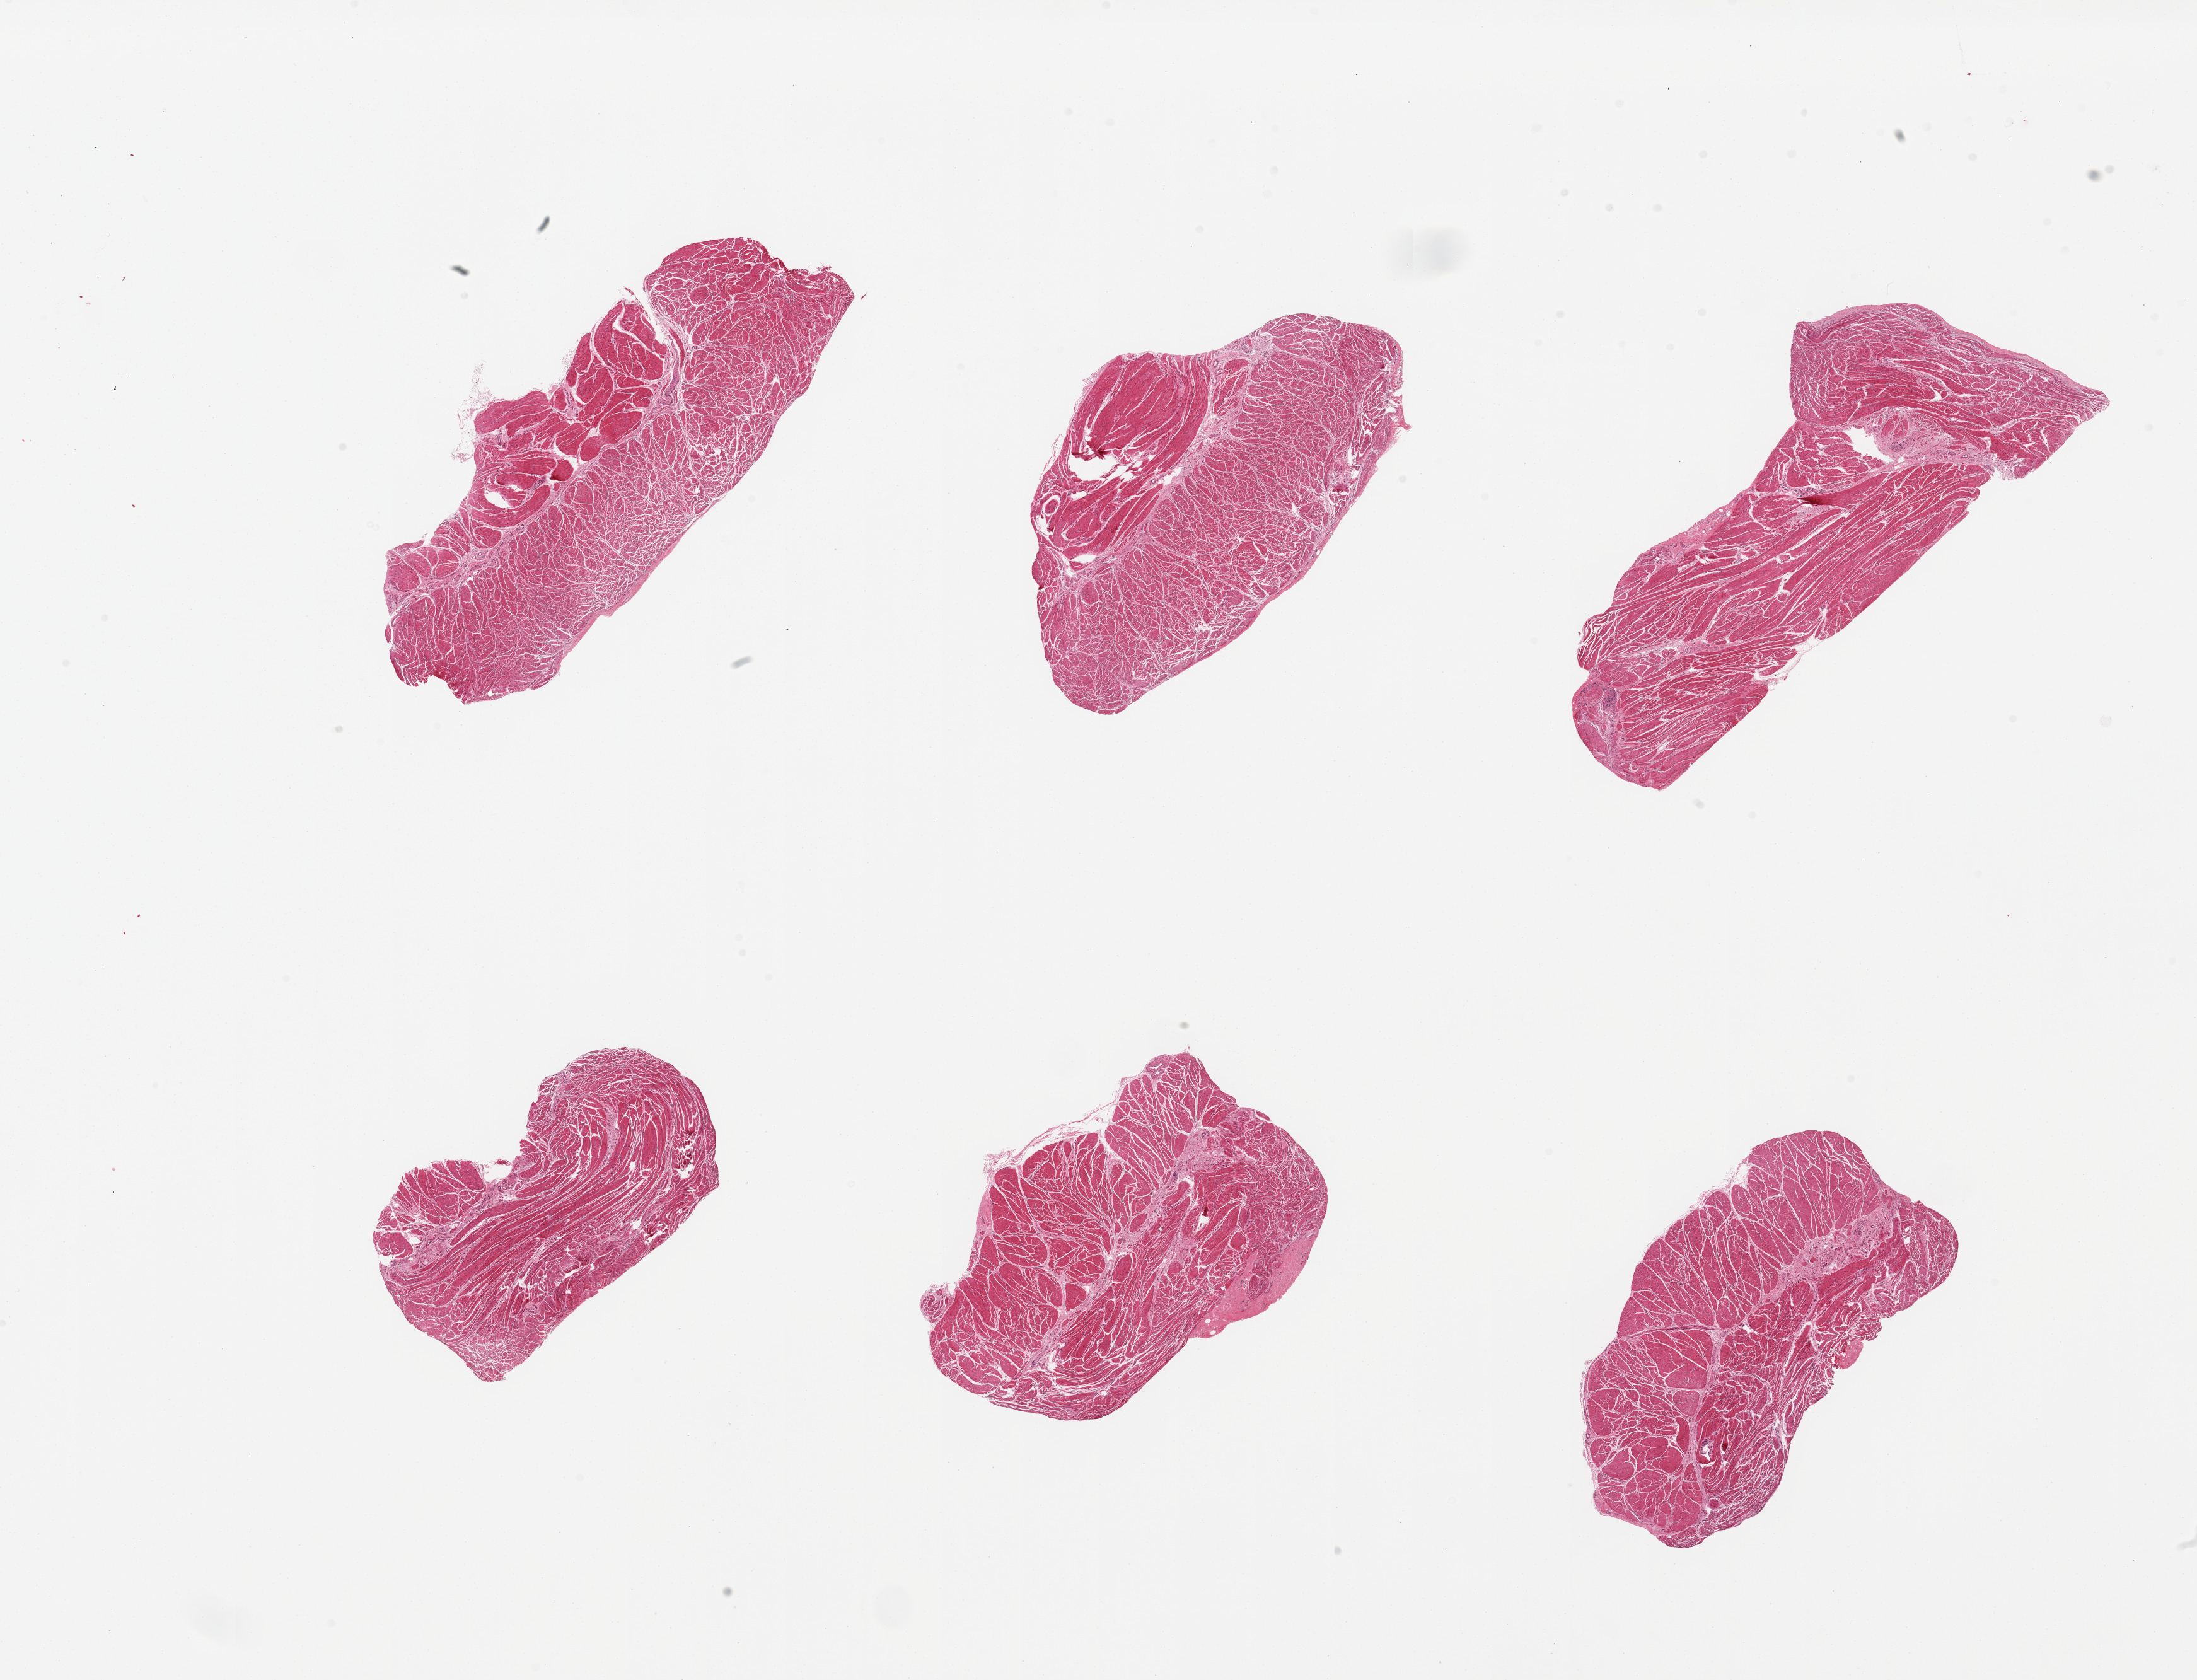
Whole-slide image, hematoxylin and eosin (H&E) stain, whole scanned area (about 27.6 x 21.1 mm) shown as a low-resolution overview; PAXgene-fixed, paraffin-embedded tissue; section of gastroesophageal junction (target tissue); donor tissue sample.
Pathologist's review note for this sample: 6 pieces, target muscularis, good specimens.